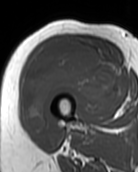
MRI of an extremity soft-tissue mass, one axial slice; slice 40 of 99 in the series (ordered by position); MR volume resampled by the dataset authors to the PET/CT grid (not the native acquisition matrix); 3.27 mm slice thickness; 138 × 172 image matrix, field of view 135 × 168 mm. Female patient. Case-level facts recorded for this patient, not image findings: histological type: pleiomorphic undifferentiated sarcoma; grade: high; site of the primary tumour: right quadricep.
Outlined on this slice (expert contour drawn on MRI and transferred to this co-registered scan by the dataset authors):
- gross tumour volume including surrounding oedema: bounding box [x1, y1, x2, y2] px = [23, 39, 118, 131]
- gross tumour volume (mass): [23, 39, 118, 131]